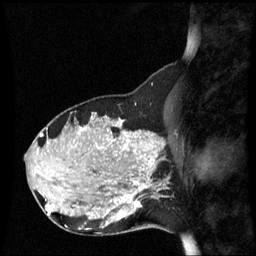
Breast MRI (dynamic contrast-enhanced), one sagittal slice; dynamic contrast-enhanced series, image 2 of 3 at this slice position (ordered by acquisition); 1.5 T; TE 4.2 ms, TR 8.9 ms; 2.2 mm slice thickness; 256 × 256 image matrix, field of view 220 × 220 mm. Female patient, age 31 years. From the clinical record (not read from this slice): setting: breast cancer imaged before/during neoadjuvant chemotherapy; receptor status: HR-positive, HER2-negative.
Structures marked on this image (semi-automatically segmented with operator editing):
- analysis volume of interest (the breast-tissue region the enhancement analysis was run in; not a lesion): bounding box (x1, y1, x2, y2) in pixels: (90, 180, 152, 235)
- tumour enhancement mask (voxels above the 70 % enhancement threshold inside the analysis volume of interest): (120, 182, 150, 219)